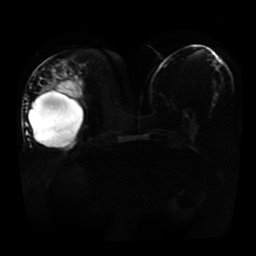
Breast MRI, one axial slice. Slice 16 of 41 in the series (ordered by position). Diffusion-weighted series; image 2 of 4 stored at this slice position (different b-values; order by instance number). 1.5 T. 5 mm slice thickness. 256 × 256 image matrix. Female patient.
Annotated regions visible in this slice (manually delineated by an expert):
- tumour on diffusion-weighted imaging: bounding box [x1, y1, x2, y2] px = [54, 82, 81, 100]